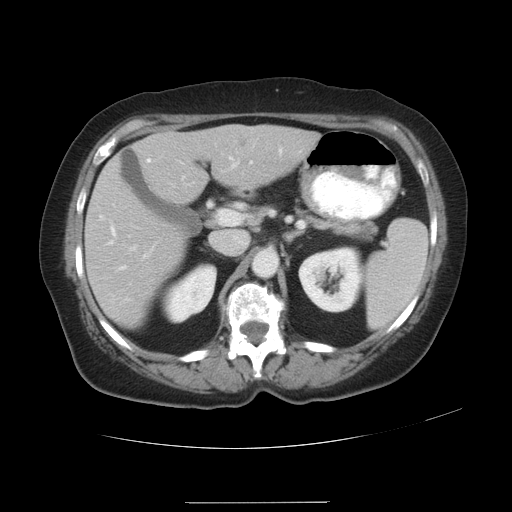
Contrast-enhanced abdominal CT, one axial slice; position 17 of 32 along the scan axis; intravenous contrast given; soft-tissue window (W 400 / L 40 HU); 7.5 mm slice thickness; 512 × 512 image matrix, field of view 386 × 386 mm. Female patient, age 65 years. Case-level facts recorded for this patient, not image findings: diagnosis: colorectal cancer liver metastases, imaged before liver resection; multiple liver metastases: yes; largest metastasis: 1.7 cm.
Structures marked on this image (outlined manually by an expert reader):
- liver: bounding box (x1, y1, x2, y2) in pixels: (86, 126, 316, 324)
- planned liver remnant (the part of the liver to remain after resection): (86, 133, 216, 325)
- portal vein (with intrahepatic branches): (110, 156, 254, 268)
- liver metastasis: (240, 140, 246, 147)